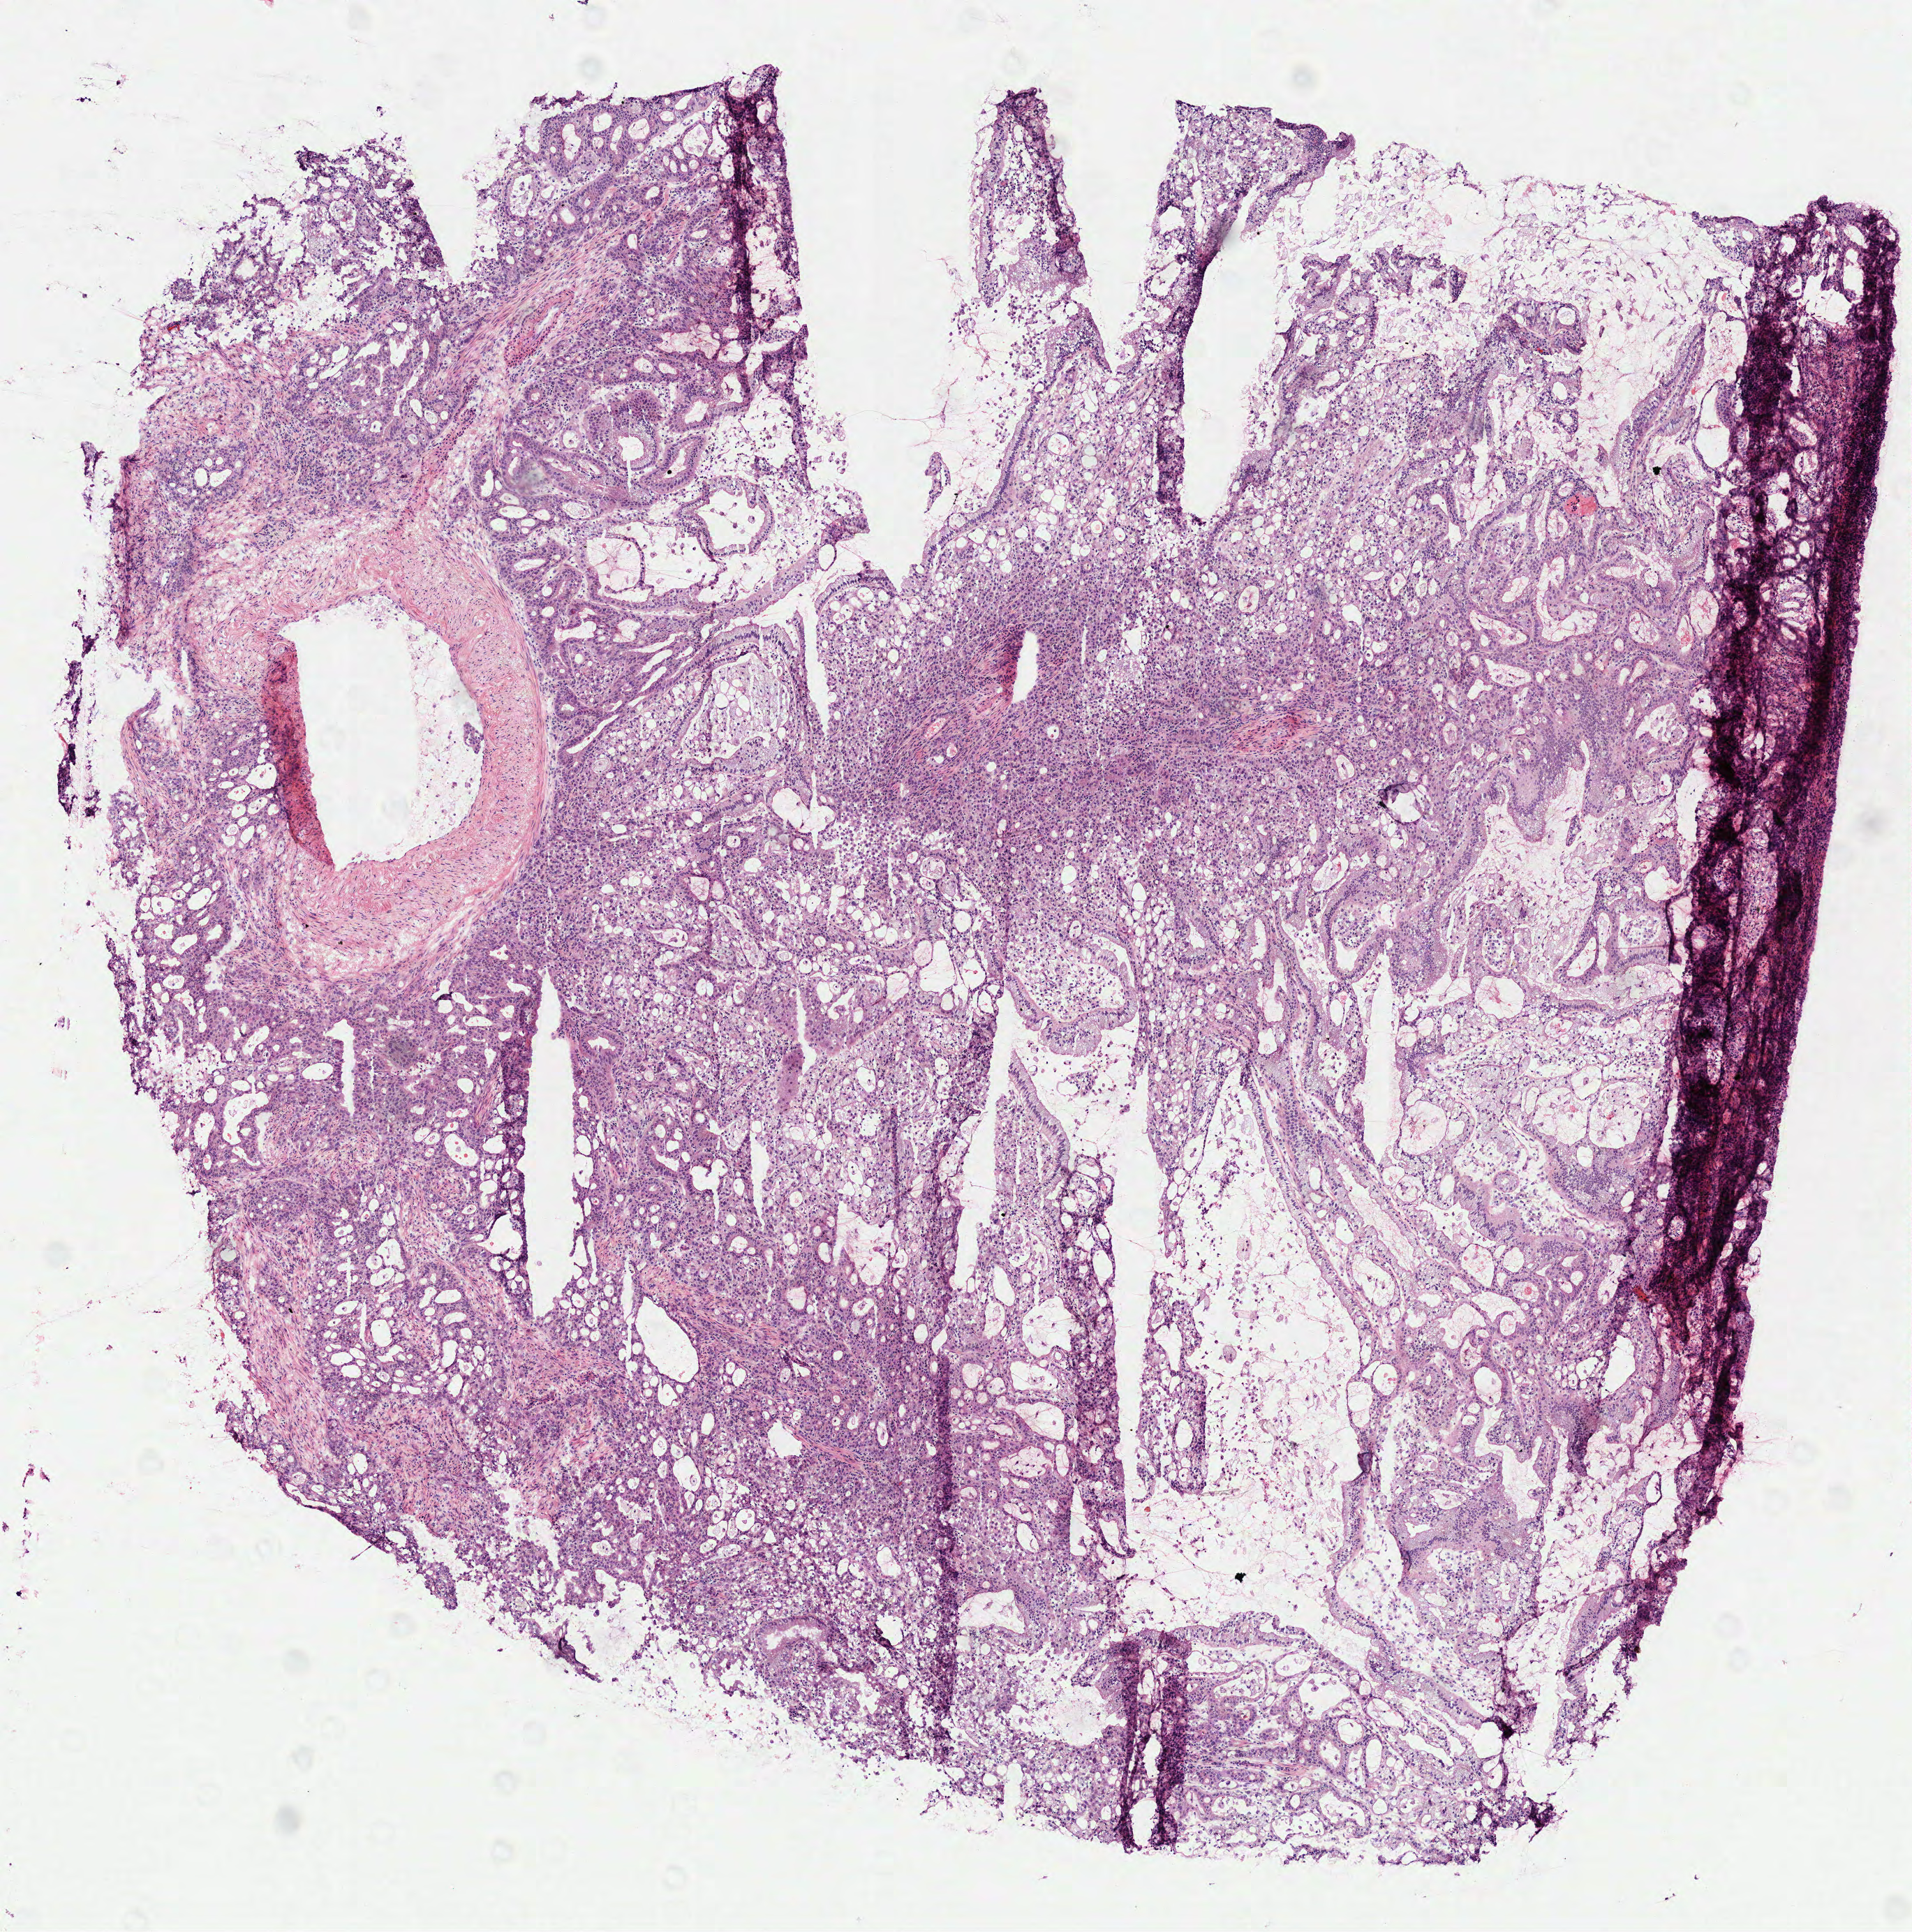
Digitized H&E tissue section (whole slide) — shown as a low-resolution overview of the whole scanned area (about 5.5 x 5.6 mm). Frozen section from the top of the tissue portion. Sample: primary tumour, stomach. Patient: male, age at initial diagnosis 75 years. Histologic grade: G3 (poorly differentiated). Slide review estimates, as recorded: tumour cells 100%, tumour nuclei 85%, normal cells 0%, stromal cells 0%, necrosis 0%. Infiltration values recorded for this section: lymphocyte infiltration 10%, monocyte infiltration 4%, neutrophil infiltration 0%.
Lymph nodes positive (case pathology): 6 of 15 examined. Histologic diagnosis: Tubular adenocarcinoma. AJCC pathologic stage: IIIA (7th edition).